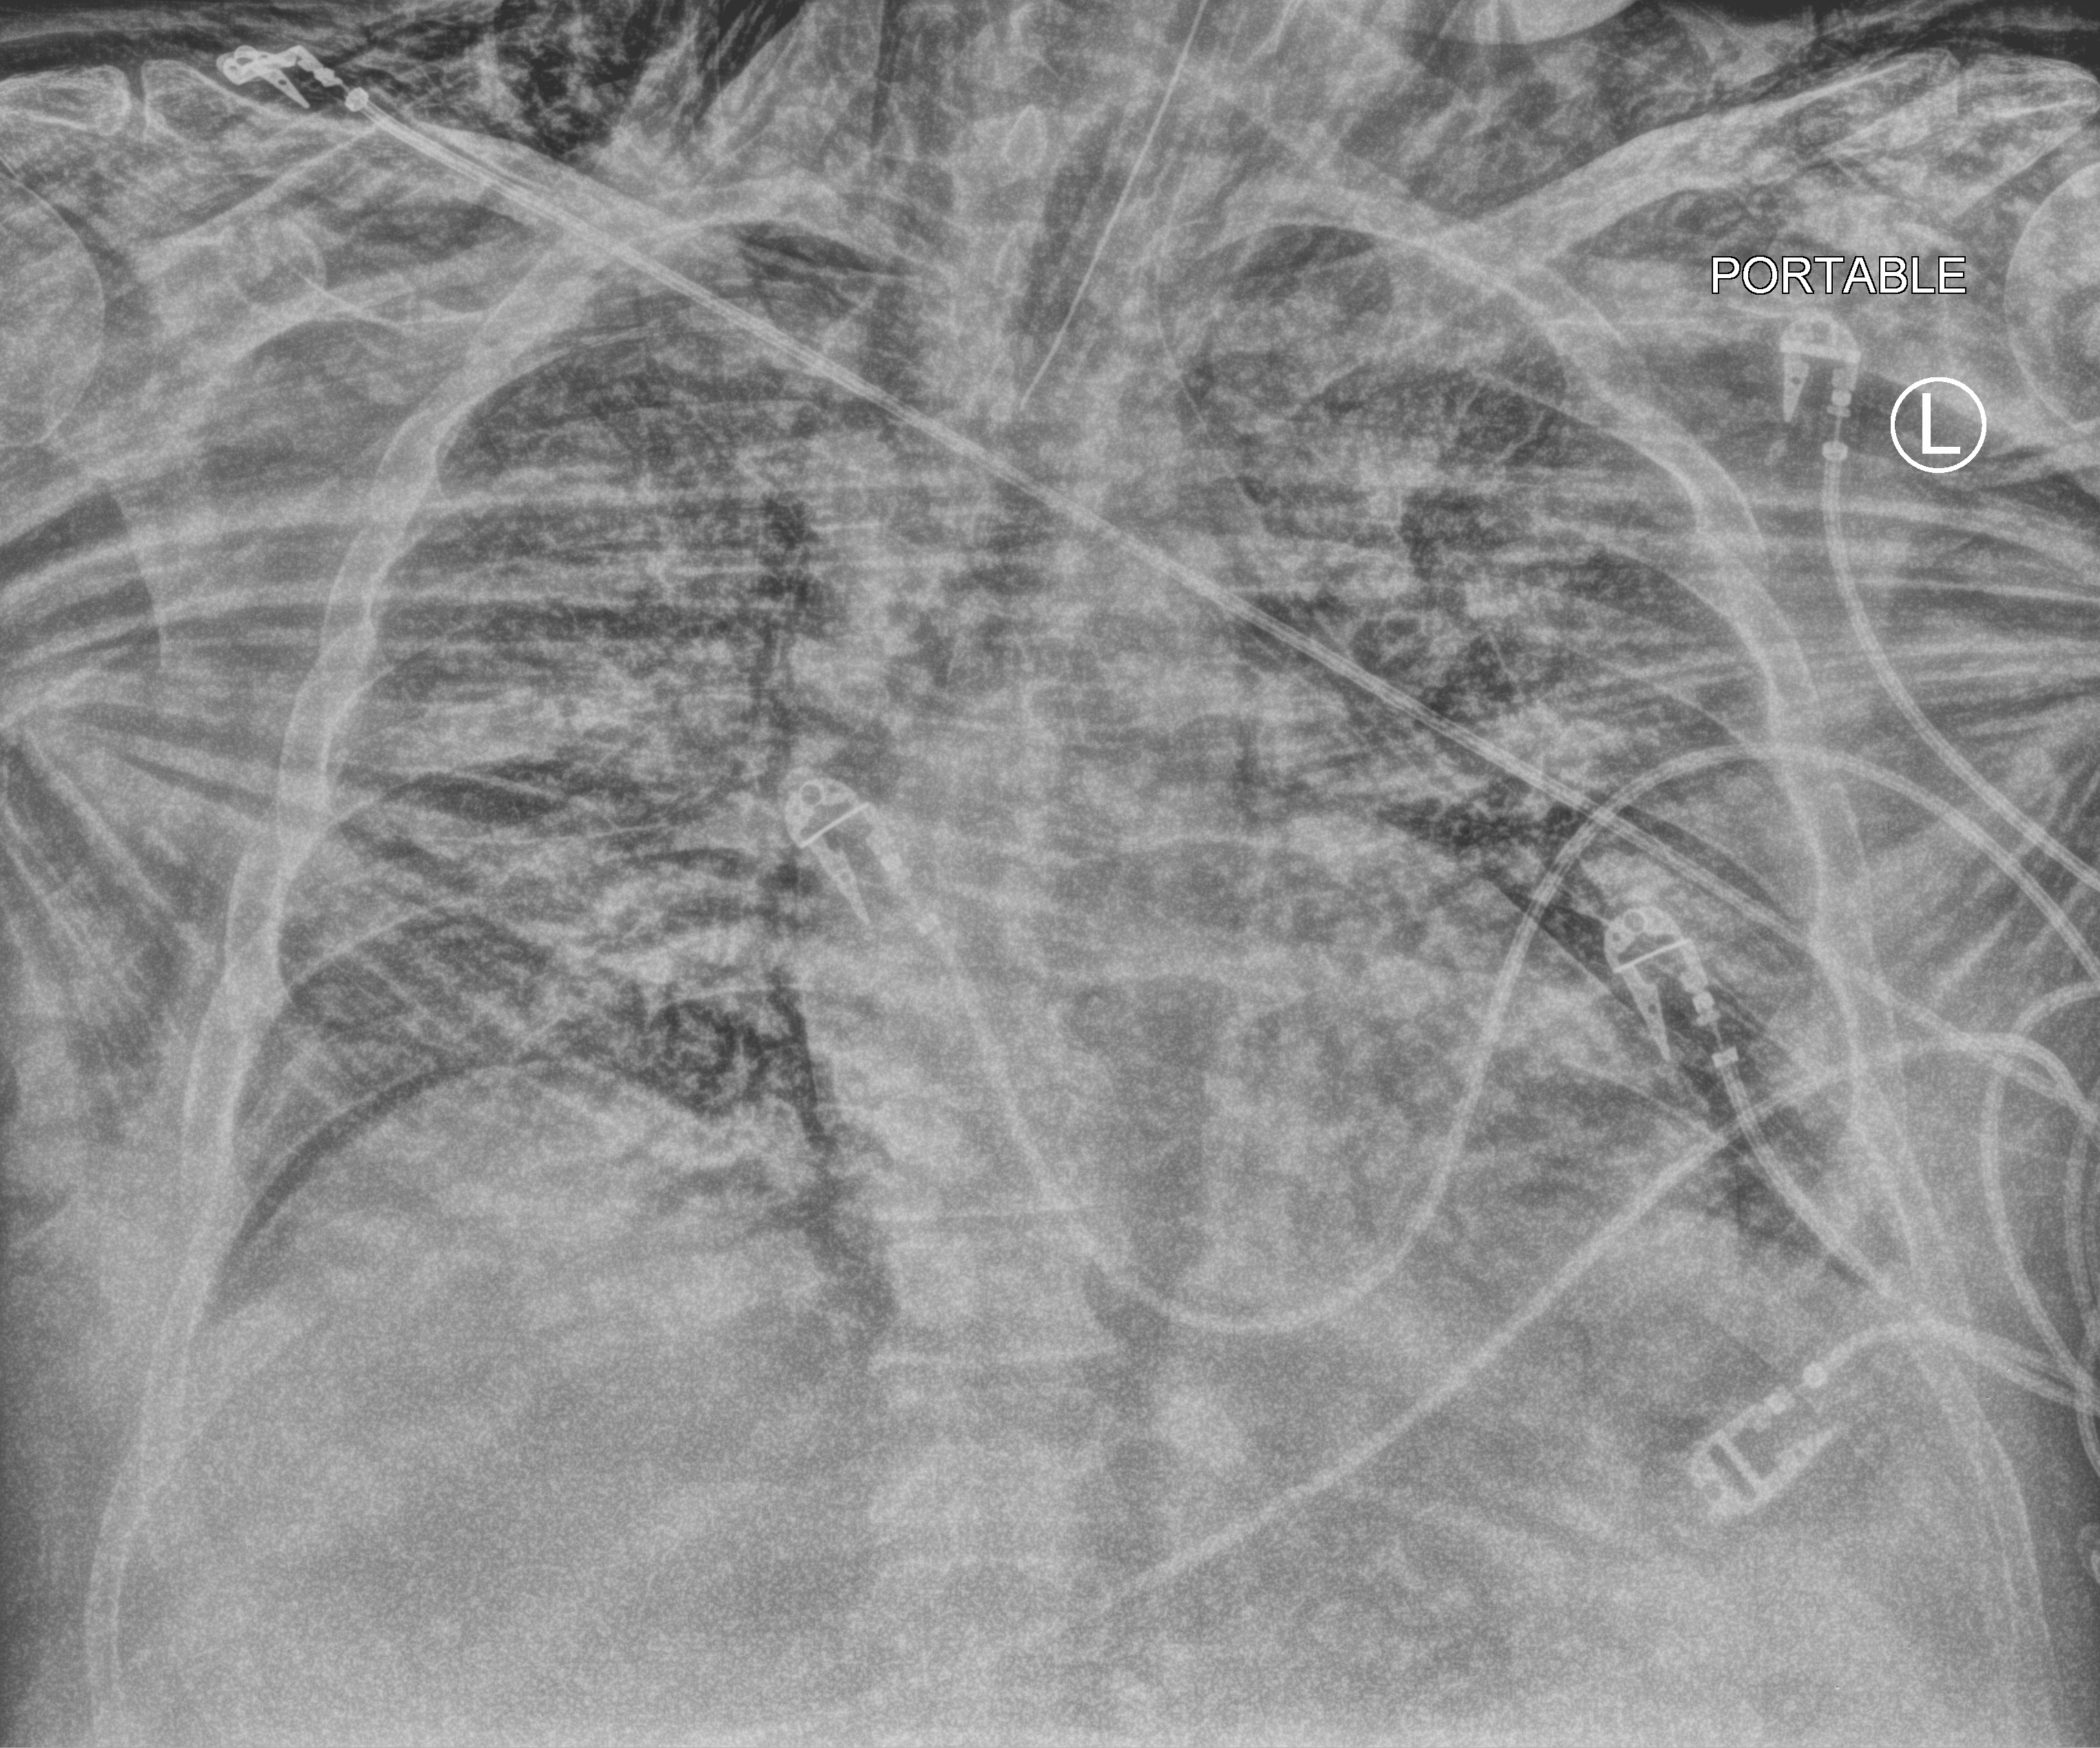
Portable chest radiograph, anteroposterior (AP) projection. Patient hospitalised with COVID-19, aged 18–59 years.
From the hospital-stay record, not from the radiograph (when in the stay this image was taken is not recorded):
- mechanically ventilated during this hospital stay: yes